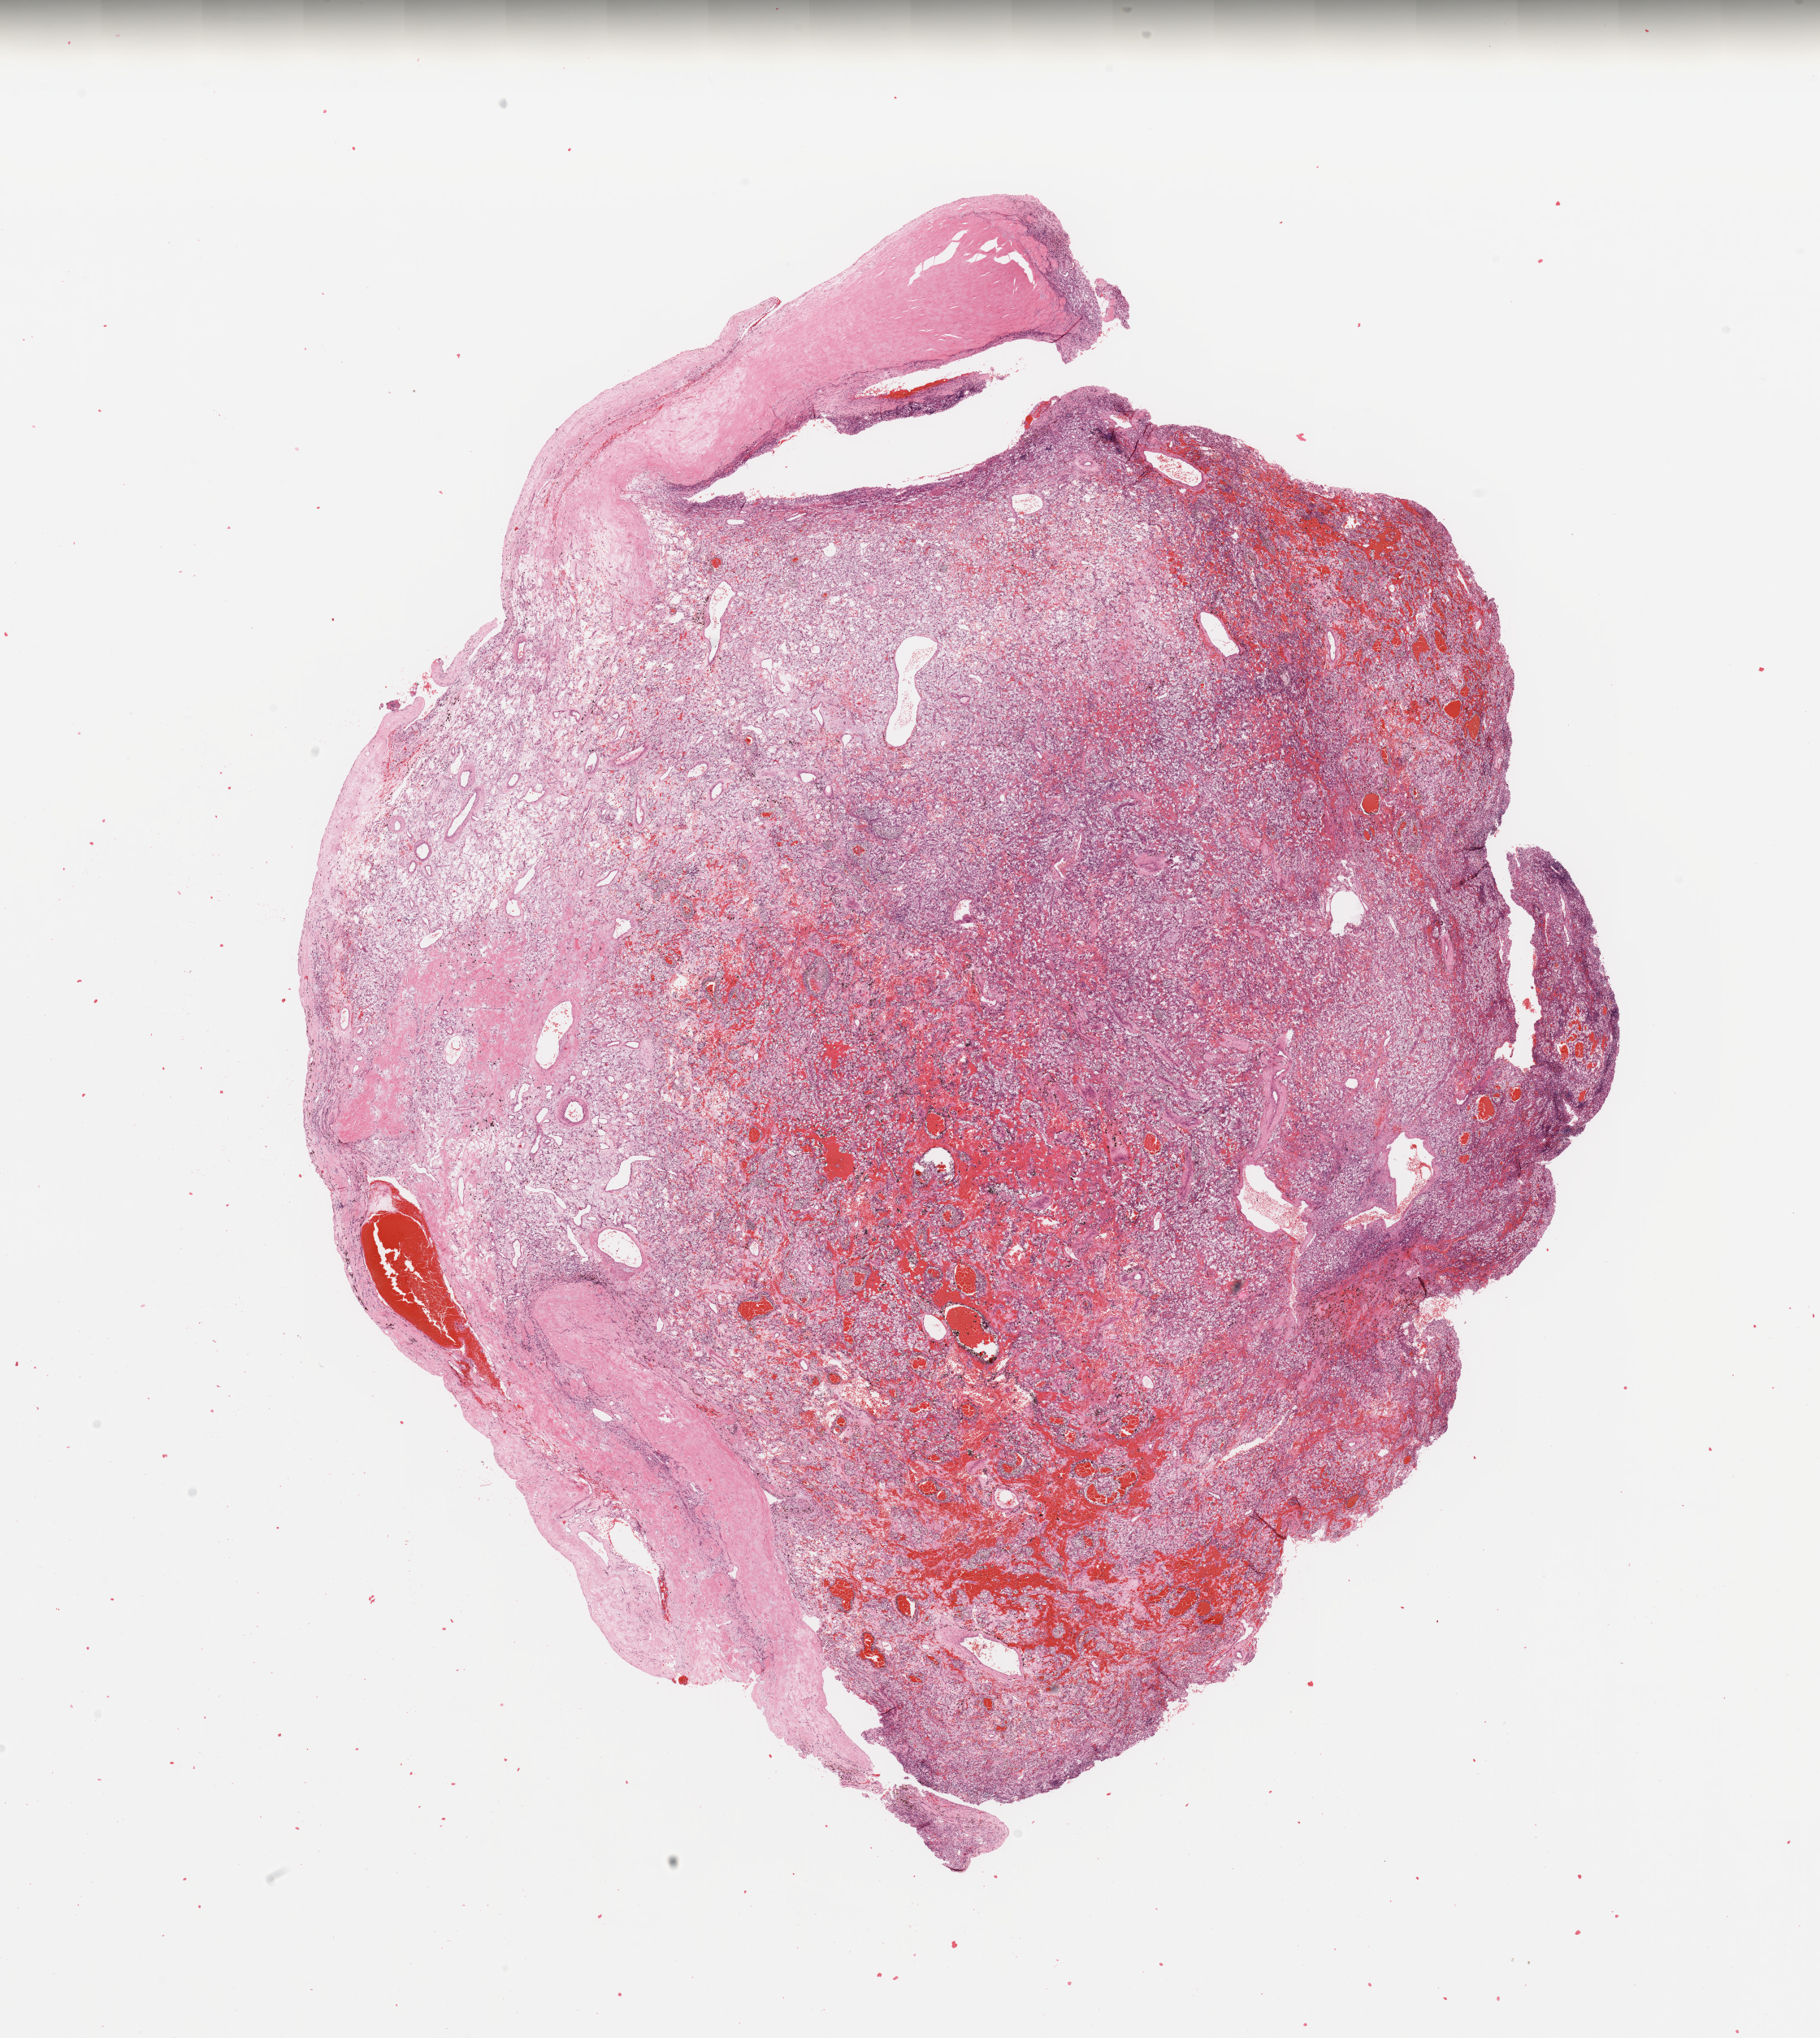
Digitized H&E-stained tissue section (whole slide) — a low-resolution overview of the entire scanned area, about 17.7 x 19.8 mm; kidney, tumour tissue. Male, 61 y/o. Histologic grade: G2 (moderately differentiated).
Histologic diagnosis: Renal cell carcinoma, NOS.